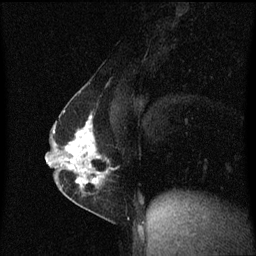
Breast MRI (dynamic contrast-enhanced), one sagittal slice; slice 32 of 60 in the series (ordered by position); dynamic contrast-enhanced series, image 2 of 3 at this slice position (ordered by acquisition); 1.5 T; TE 4.2 ms, TR 8.4 ms; 2 mm slice thickness; 256 × 256 image matrix, field of view 200 × 200 mm. Female patient, age 40 years.
Outlined on this slice (semi-automatic segmentation, software-assisted and operator-edited):
- analysis volume of interest (the breast-tissue region the enhancement analysis was run in; not a lesion): box from (x=57, y=110) to (x=112, y=191) px
- tumour enhancement mask (voxels above the 70 % enhancement threshold inside the analysis volume of interest): (x=65, y=116)–(x=108, y=189)